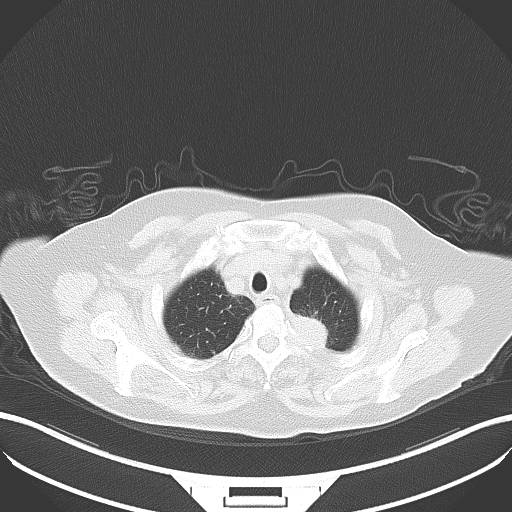
Chest CT, one axial slice. Position 36 of 42 along the scan axis. 100 kVp. Lung window (W 1500 / L -600 HU). 512 × 512 image matrix. Patient: female, 81 years. From the clinical record (not read from this slice): clinical TNM (as recorded): T2a N0 M0.
Outlined on this slice (rectangle marked by the reading radiologist):
- lung tumour (recorded histology: adenocarcinoma): bounding box [x1, y1, x2, y2] px = [286, 312, 341, 355]